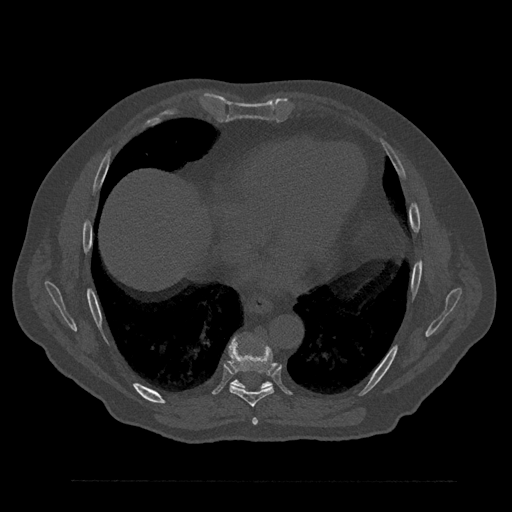
CT including the spine, one axial slice. Position 442 of 797 along the scan axis. Reconstruction kernel Br40s/3. 120 kVp. Bone window (W 1800 / L 400 HU). 512 × 512 image matrix, field of view 430 × 430 mm. Male patient, age 61 years. Case-level facts recorded for this patient, not image findings: primary cancer: prostate.
Structures marked on this image (semi-automatically segmented with operator editing):
- T7 vertebra: bounding box [x1, y1, x2, y2] px = [252, 418, 258, 425]
- T8 vertebra: [228, 341, 277, 407]
- T9 vertebra: [231, 380, 272, 389]